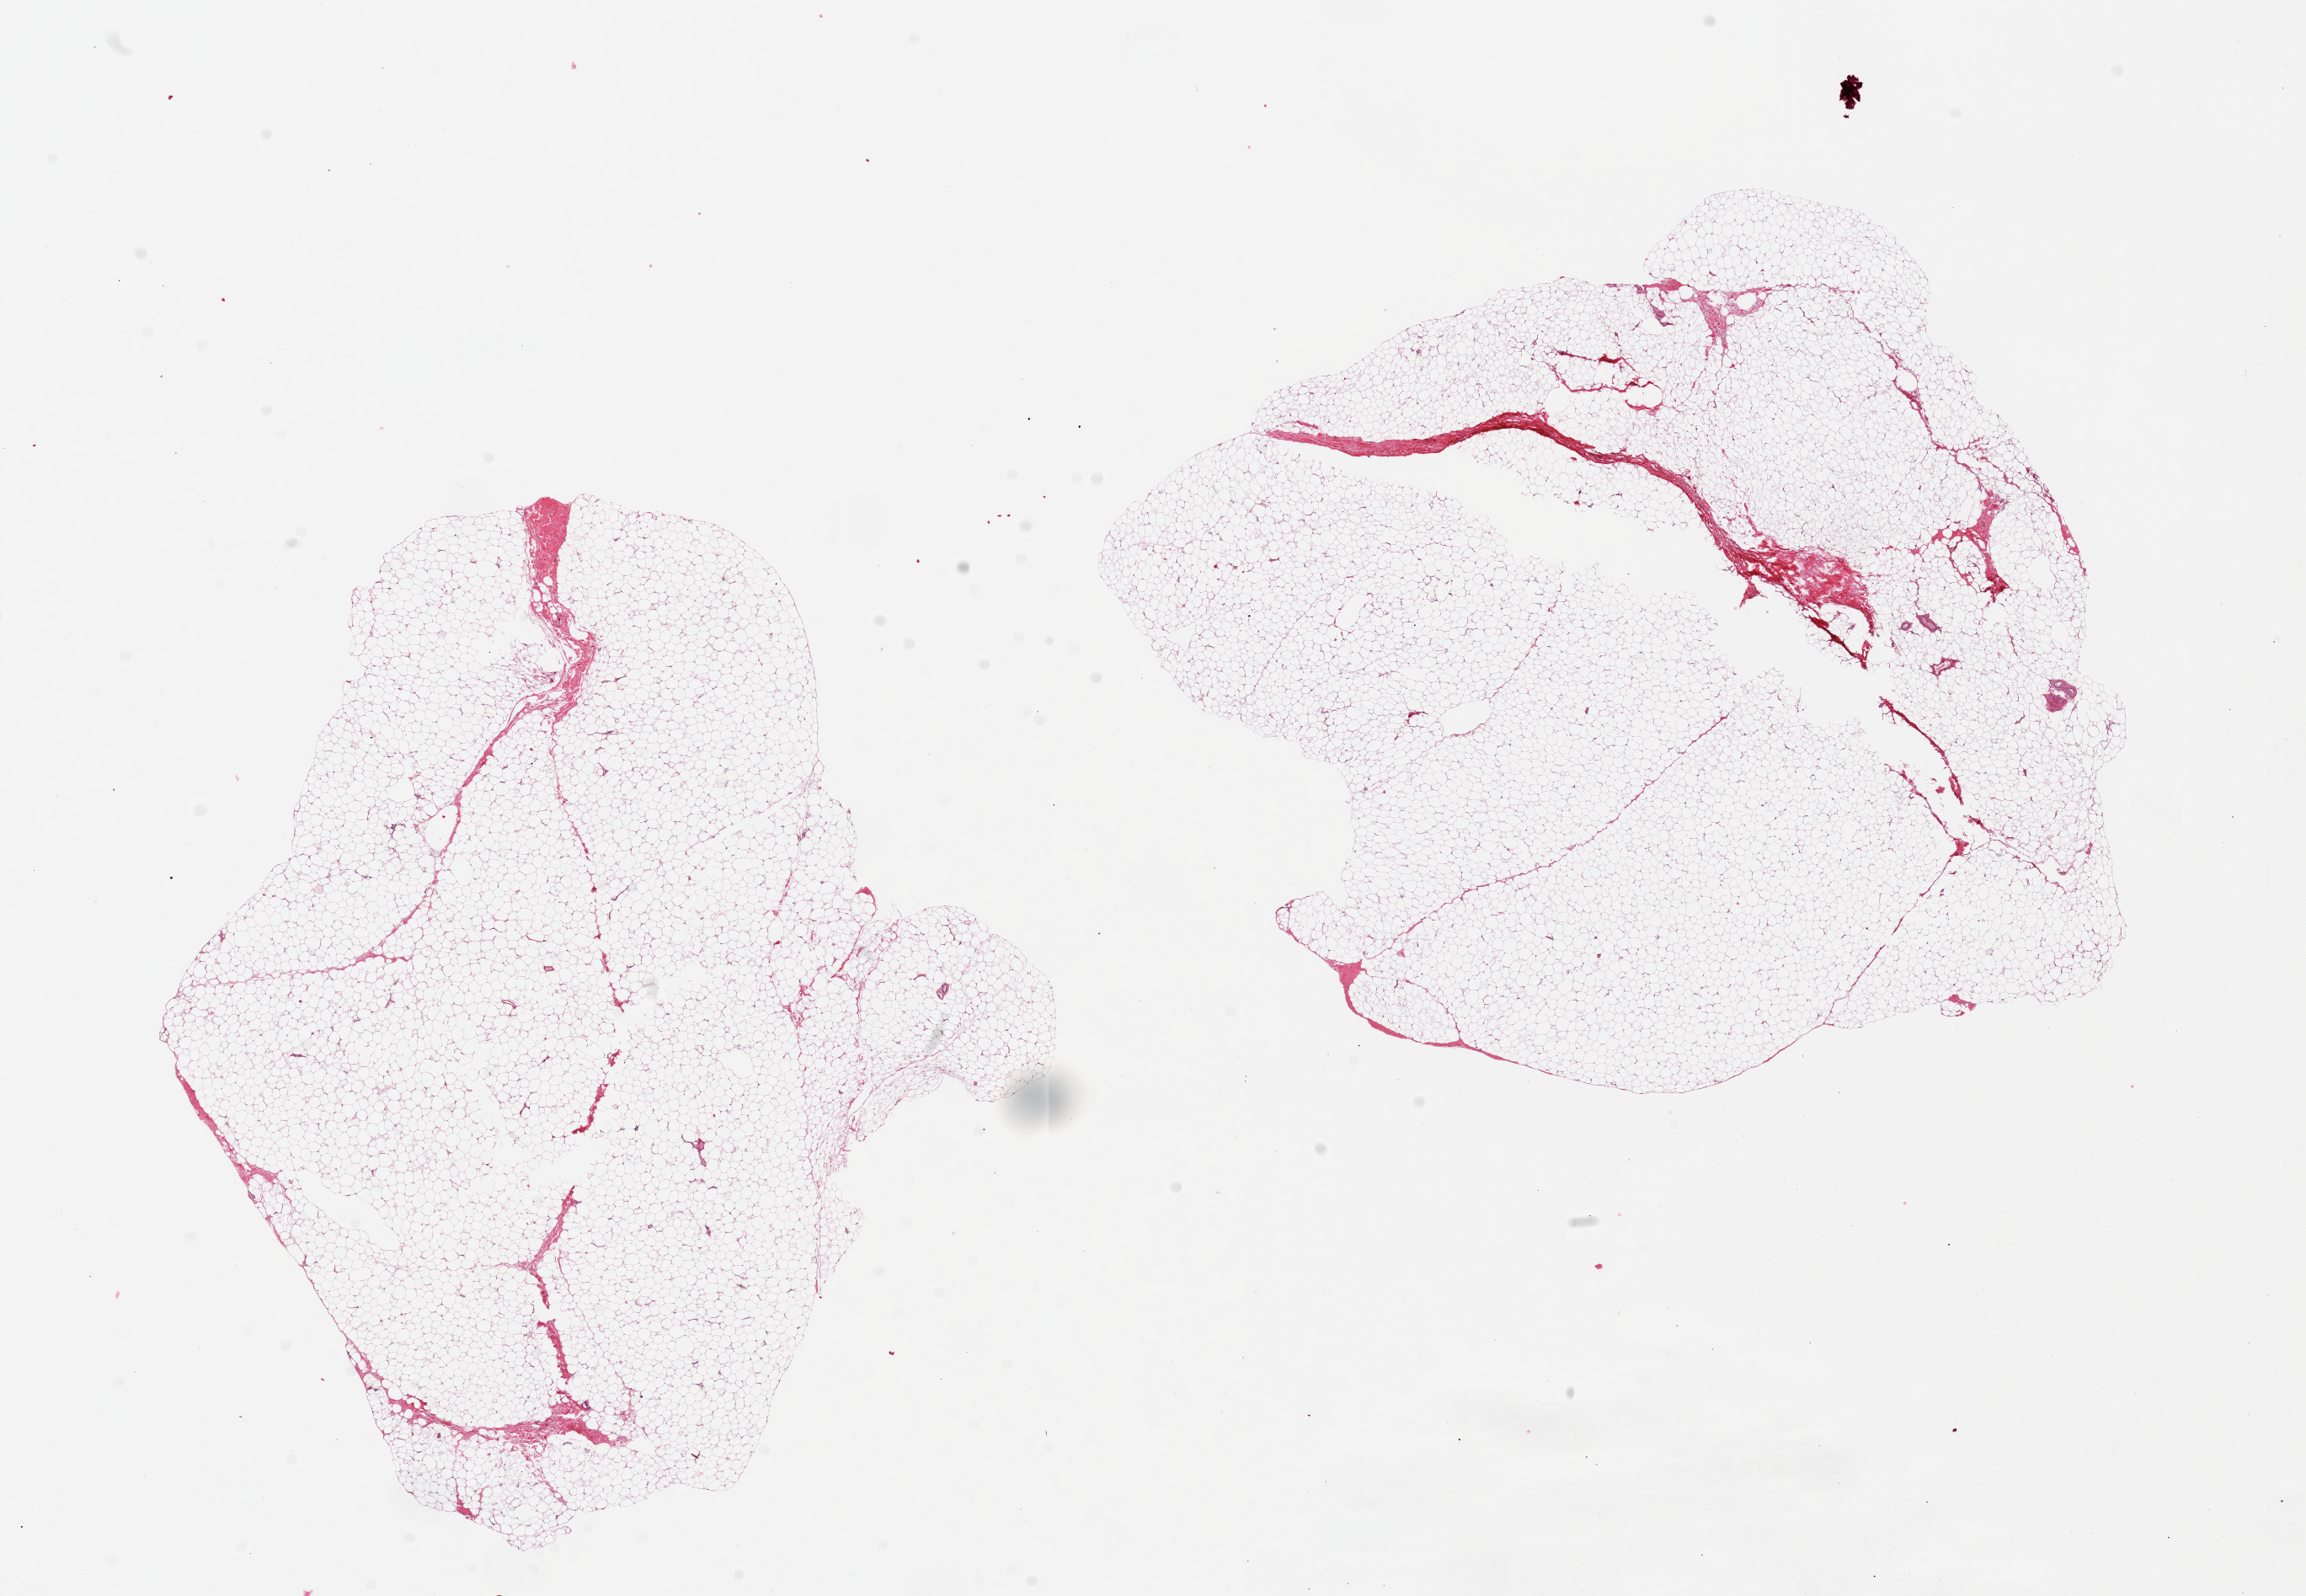
Digitized haematoxylin and eosin-stained section — shown as a low-resolution overview of the whole scanned area (about 21.7 x 15.0 mm). PAXgene-fixed paraffin-embedded (PFPE) section. Section of breast (target tissue). Donor tissue sample. Donor sex: male.
Review note (as recorded): 2 pieces ~10x8mm, no ductal elements noted.